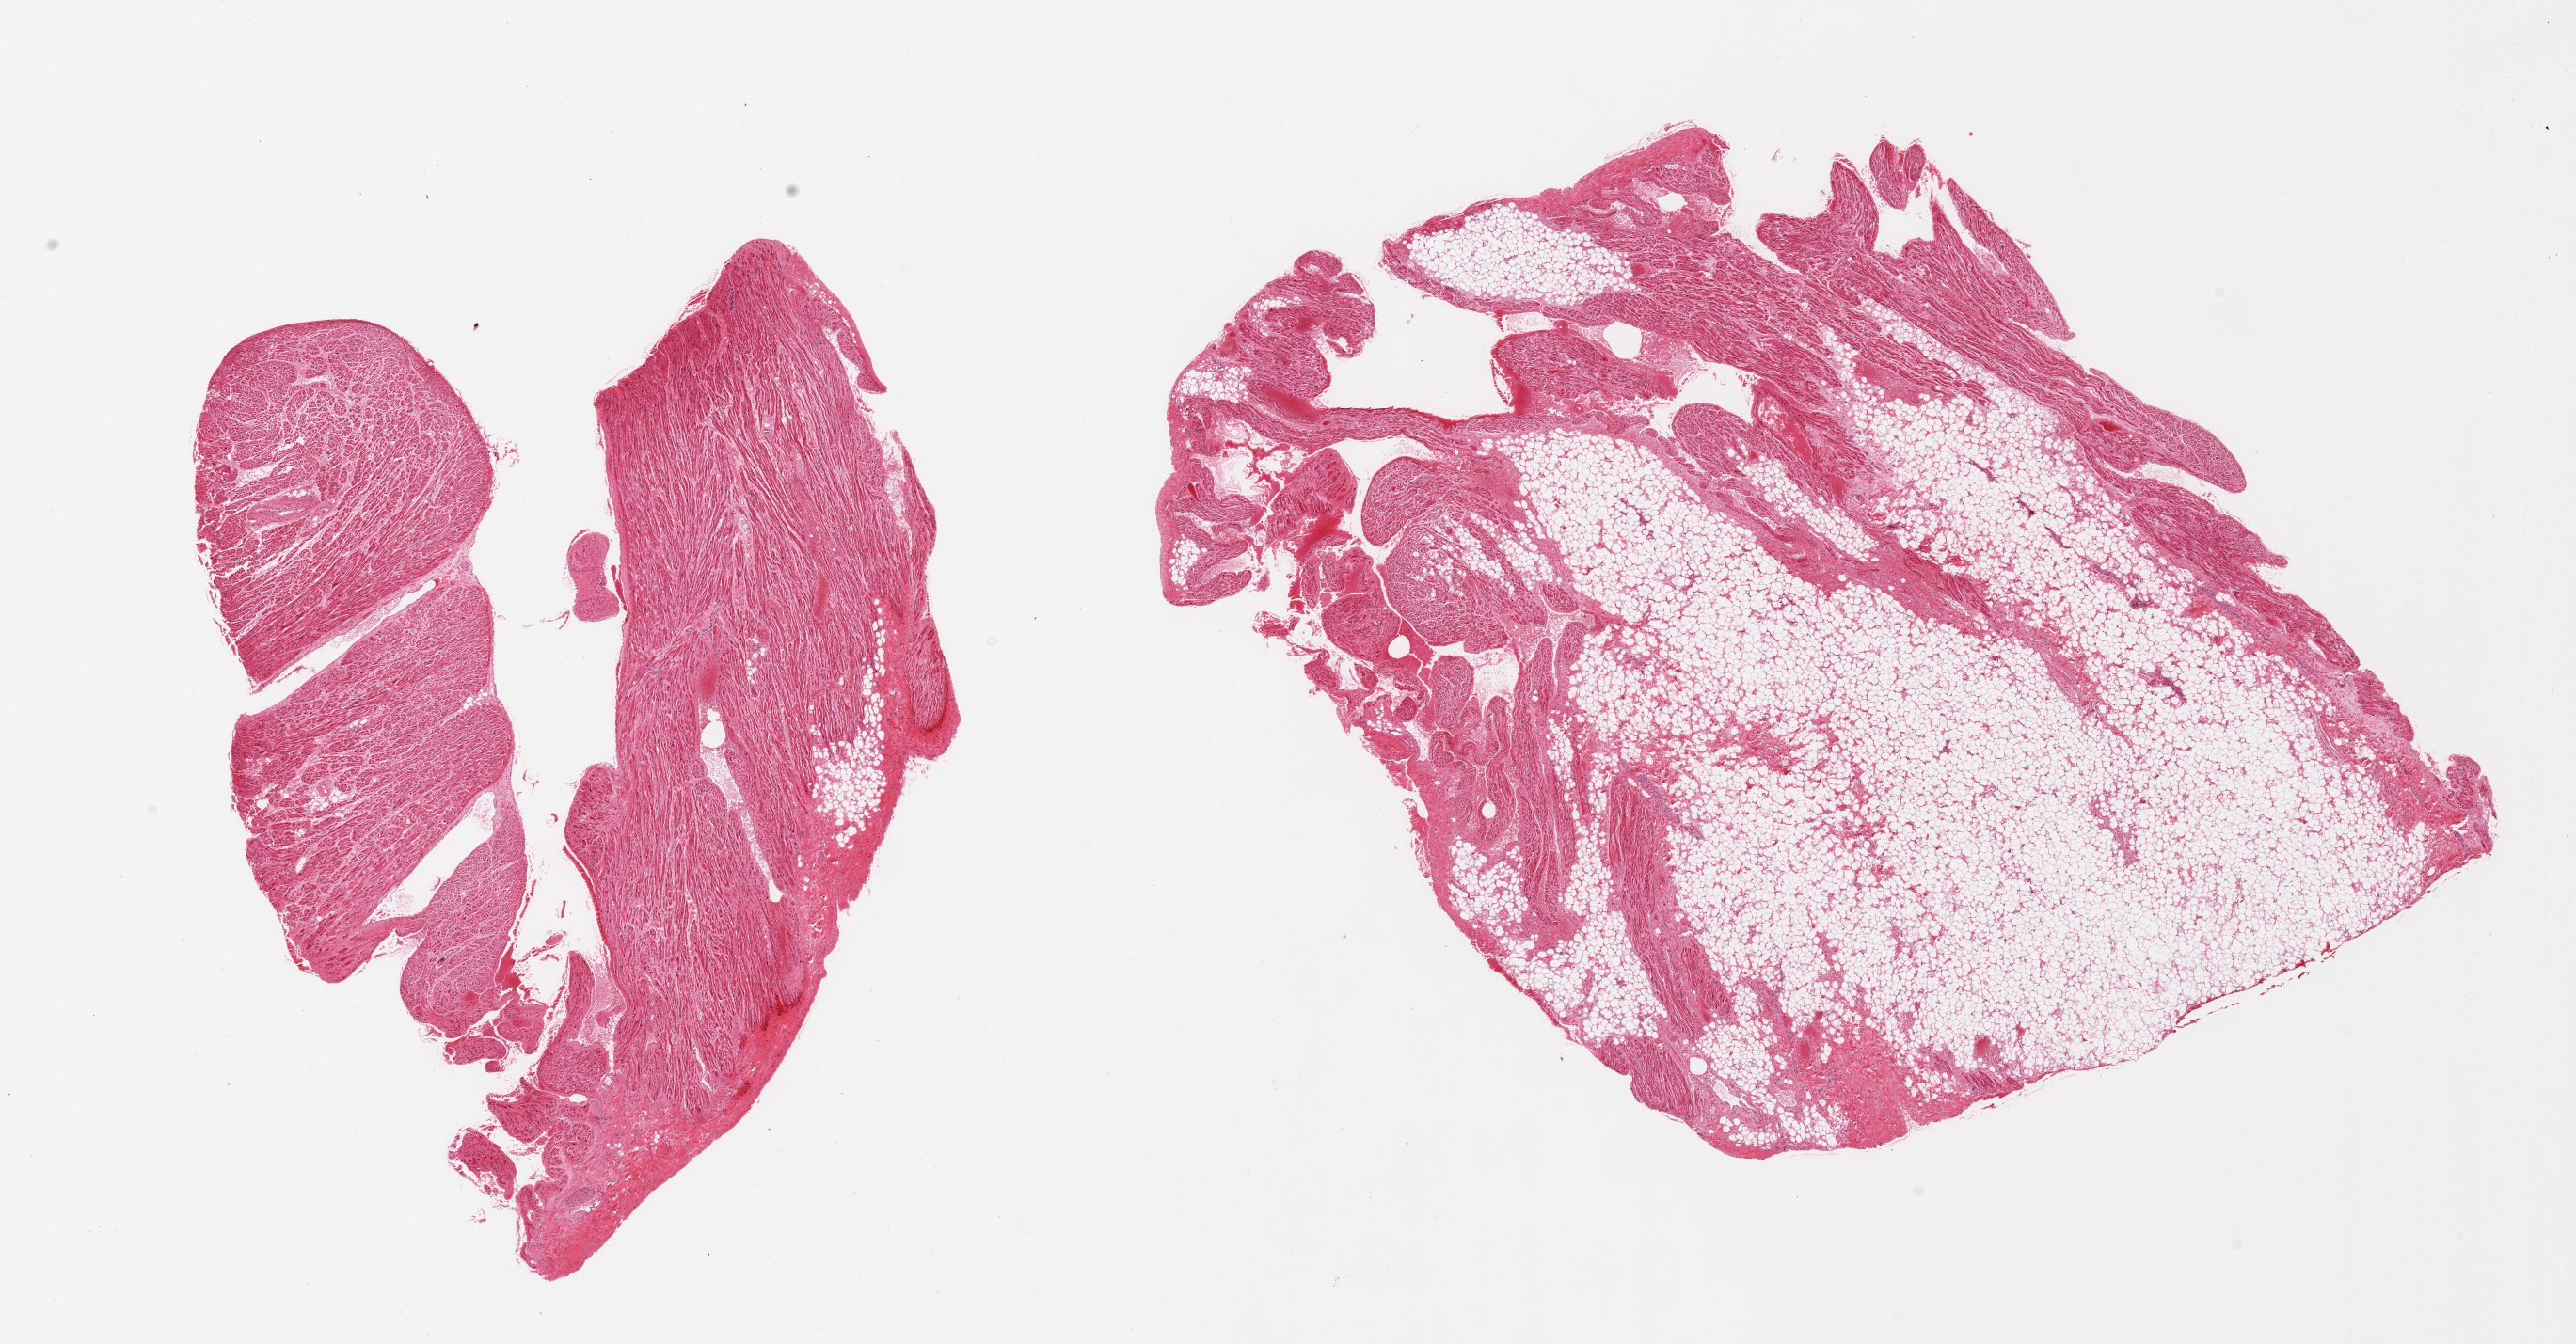
Whole-slide image, hematoxylin and eosin (H&E) stain, brightfield — a low-resolution overview of the entire scanned area, about 21.7 x 11.3 mm (acquisition: 20x scan); PAXgene-fixed, paraffin-embedded tissue; section of auricular appendage (target tissue); tissue donor sample. Donor sex: male.
Pathologist's review note for this sample: 2 pieces, significant adipose component (~30-40 %).